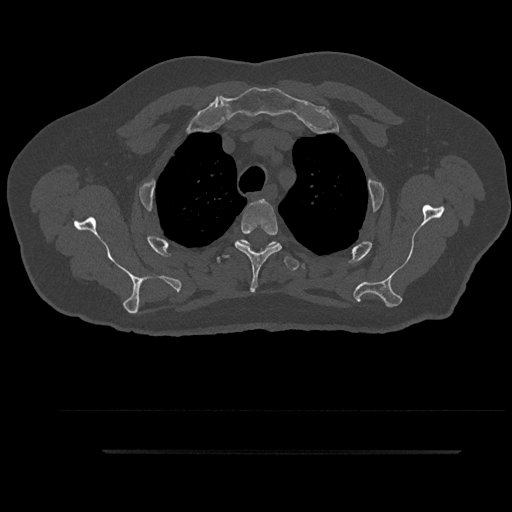
CT including the spine, one axial slice; slice 709 of 797 in the series (ordered by position); reconstruction kernel Br40s/3; 120 kVp; bone window (W 1800 / L 400 HU); 0.5 mm slice thickness; 512 × 512 image matrix, field of view 432 × 432 mm. Patient: male, 63 years. From the clinical record (not read from this slice): primary cancer: renal; vertebrae with lytic lesions (as recorded): T8.
Annotated regions visible in this slice (semi-automatic segmentation, software-assisted and operator-edited):
- T3 vertebra: bounding box <235,199,282,292> (left, top, right, bottom; pixels)
- T4 vertebra: <216,240,299,271>